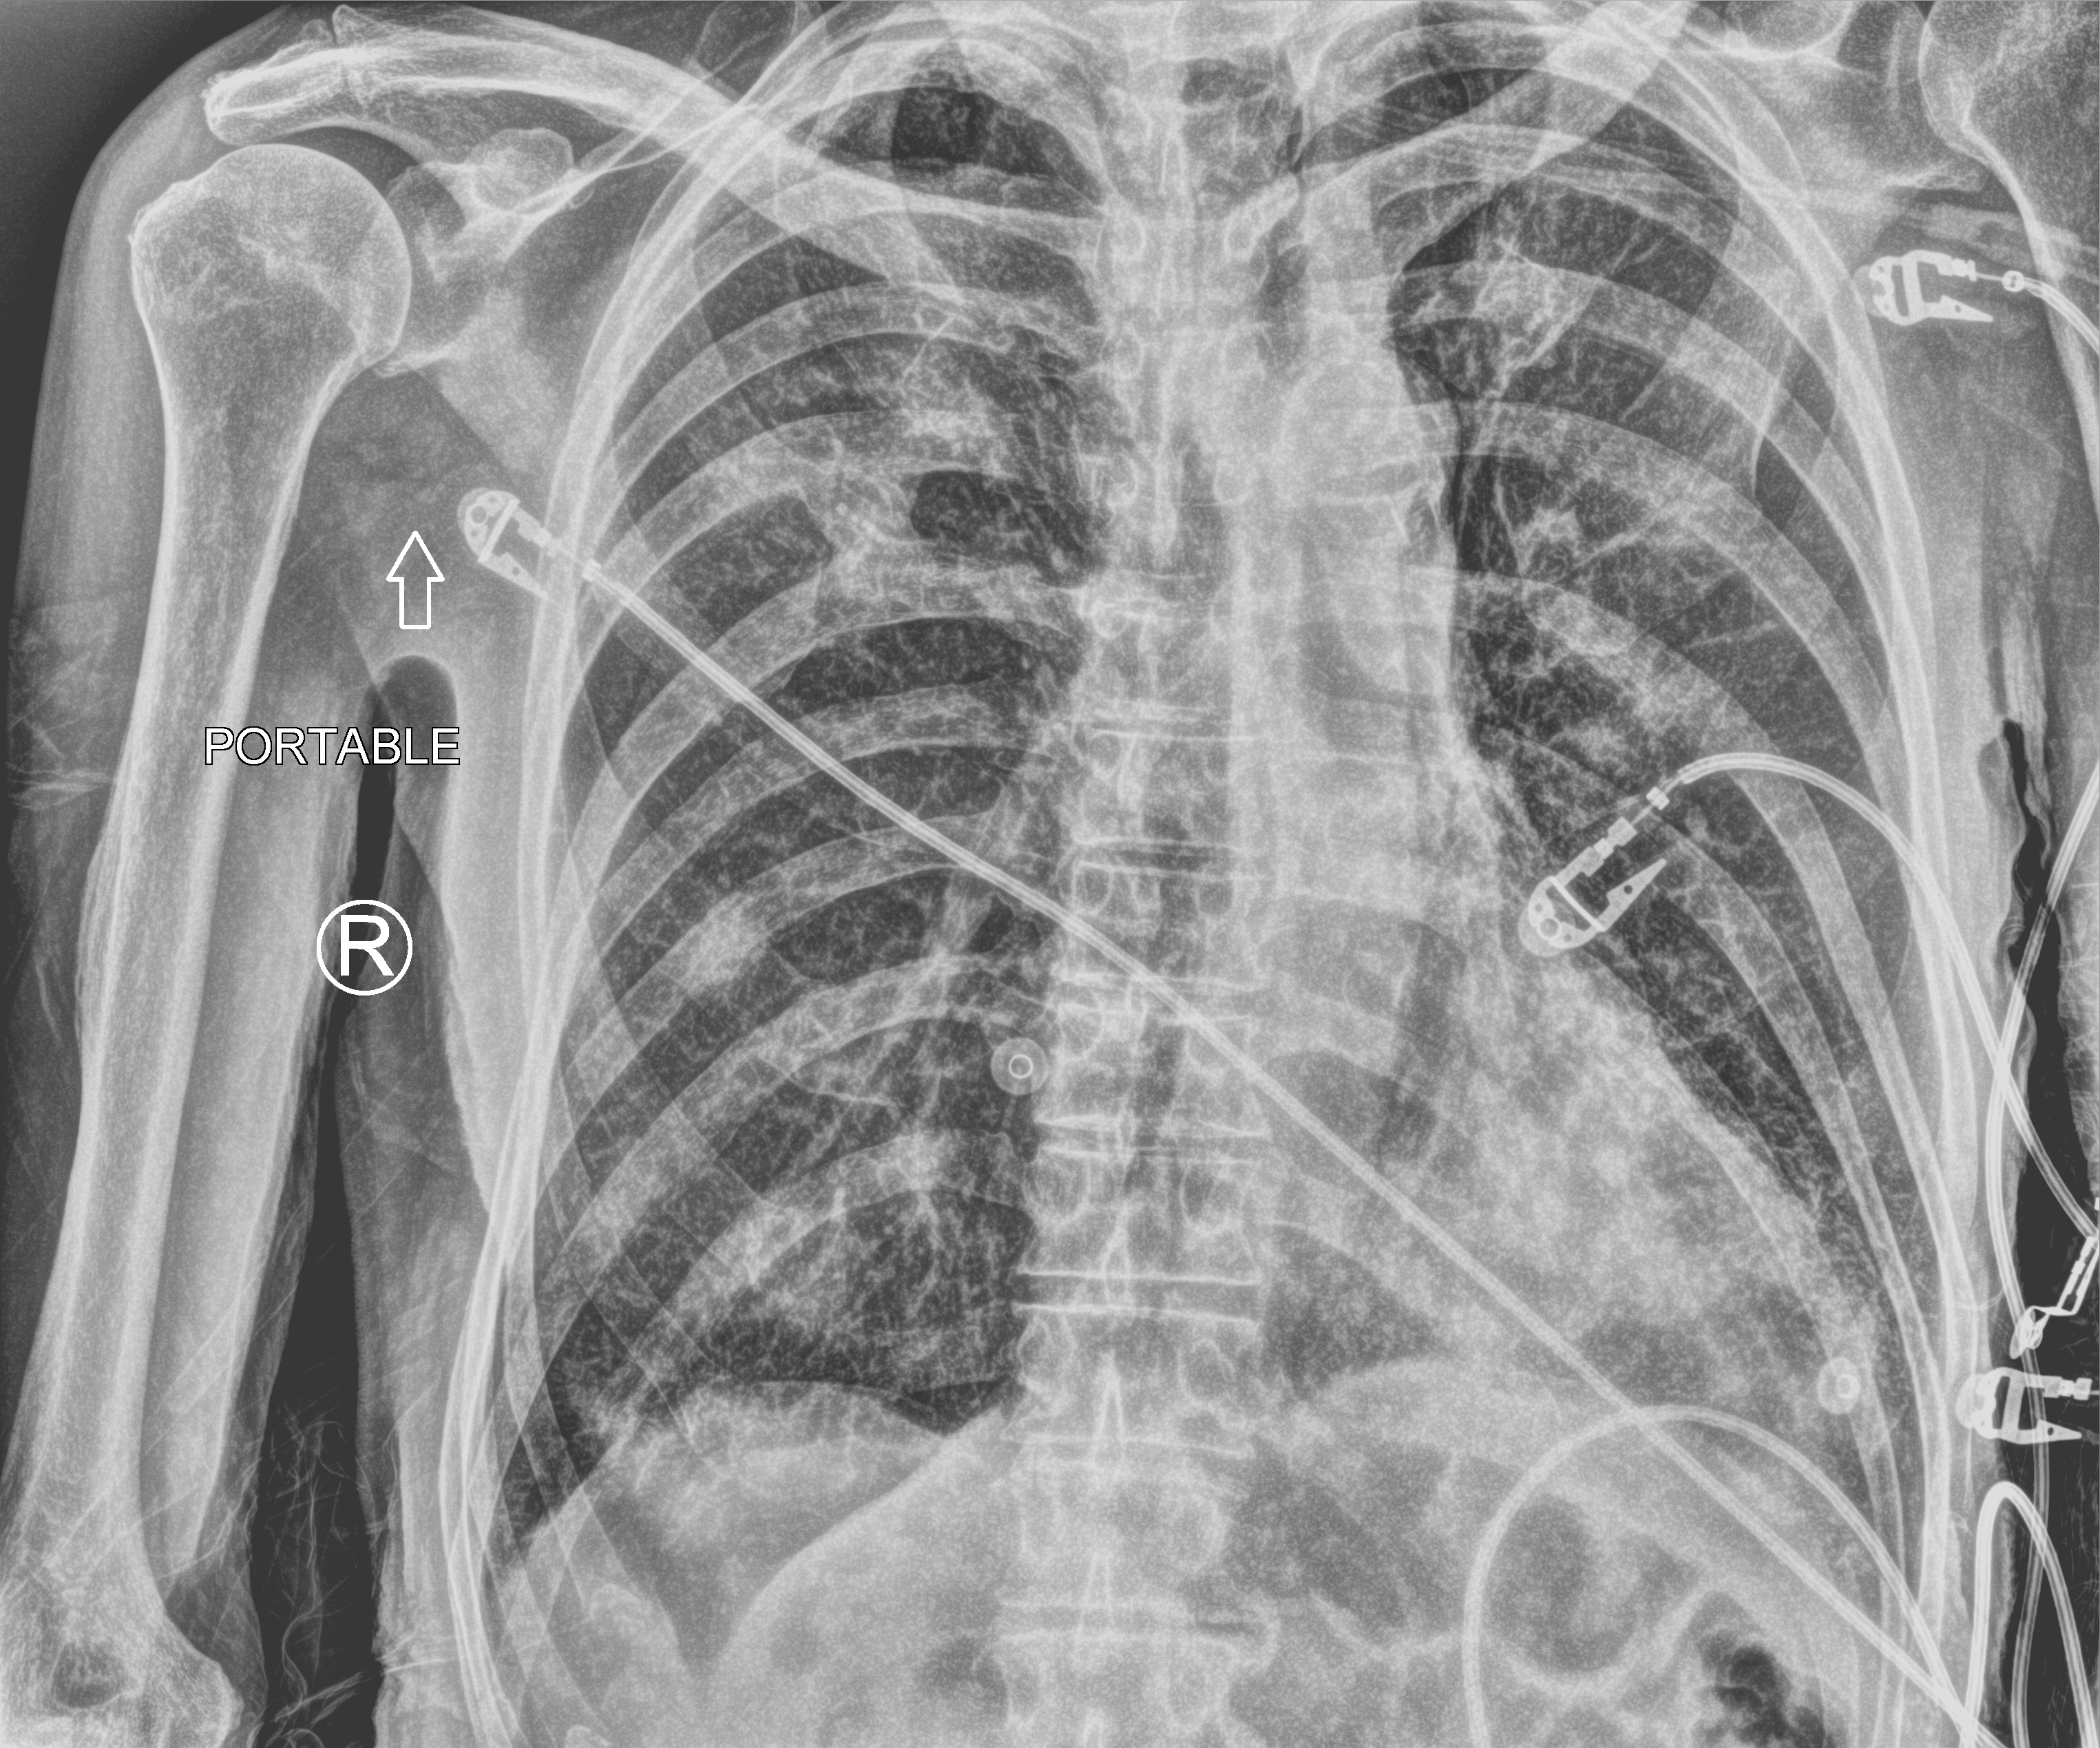
Bedside chest radiograph (computed radiography); anteroposterior (AP) projection. Male patient hospitalised with COVID-19, age 75–90 years.
Admission-level facts for this patient (not findings on this image; timing relative to this image not recorded):
- length of hospital stay: 8 days
- mechanically ventilated during this hospital stay: no